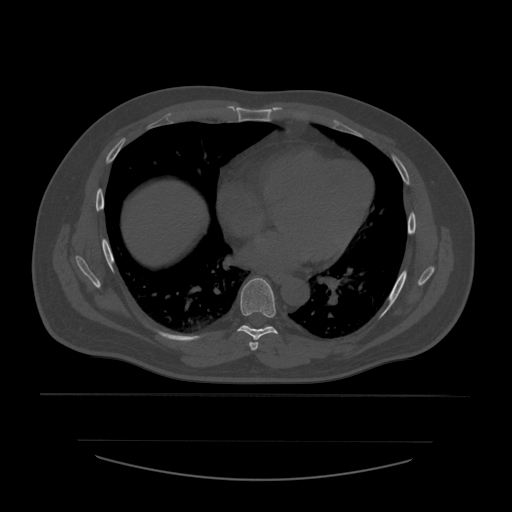
CT including the spine, one axial slice. Slice 357 of 532 in the series (ordered by position). Reconstruction kernel STANDARD. 120 kVp. Bone window (W 1800 / L 400 HU). 1.25 mm slice thickness. 512 × 512 image matrix, field of view 441 × 441 mm. Patient age 44 years. From the clinical record (not read from this slice): primary cancer: soft tissue sarcoma.
Structures marked on this image (semi-automatic segmentation, software-assisted and operator-edited):
- T6 vertebra: bounding box (x1, y1, x2, y2) in pixels: (249, 342, 259, 352)
- T7 vertebra: (237, 278, 278, 341)